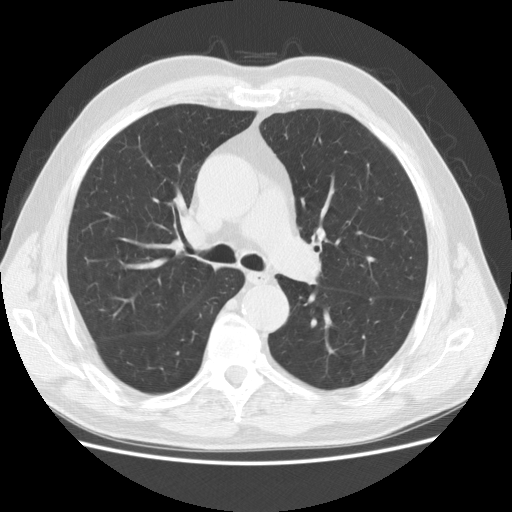
Chest CT (low-dose screening protocol), one axial image. Baseline screening round. Lung window (W 1500 / L -600 HU). 2.5 mm slice thickness. Slice 62 of 155 in the series. Male, age 73 years at enrolment. Current smoker at enrolment.
Expert reader's lesion annotation, bounding box [x1, y1, x2, y2] px = [348, 286, 400, 322]. No non-calcified nodule or mass ≥4 mm was recorded by the screening reader at this exam. Later outcome: lung cancer diagnosed 536 days after this screen — adenocarcinoma, NOS, left lower lobe, poorly differentiated (G3), stage IIA (AJCC 6th edition), 12 mm at pathology.